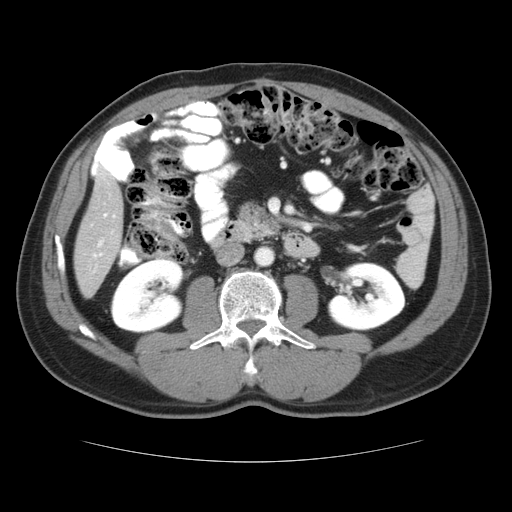
Contrast-enhanced abdominal CT, one axial slice. Slice 11 of 37 in the series (ordered by position). Reconstruction kernel STANDARD. Intravenous contrast given. Soft-tissue window (W 400 / L 40 HU). 5 mm slice thickness. 512 × 512 image matrix, field of view 374 × 374 mm. Male patient, age 66 years. Case-level facts recorded for this patient, not image findings: diagnosis: colorectal cancer liver metastases, imaged before liver resection; multiple liver metastases: yes; largest metastasis: 1.6 cm; disease in both lobes: yes.
Outlined on this slice (outlined manually by an expert reader):
- hepatic veins: bounding box <97,213,116,248> (left, top, right, bottom; pixels)
- liver: <74,167,125,297>
- planned liver remnant (the part of the liver to remain after resection): <74,174,125,297>